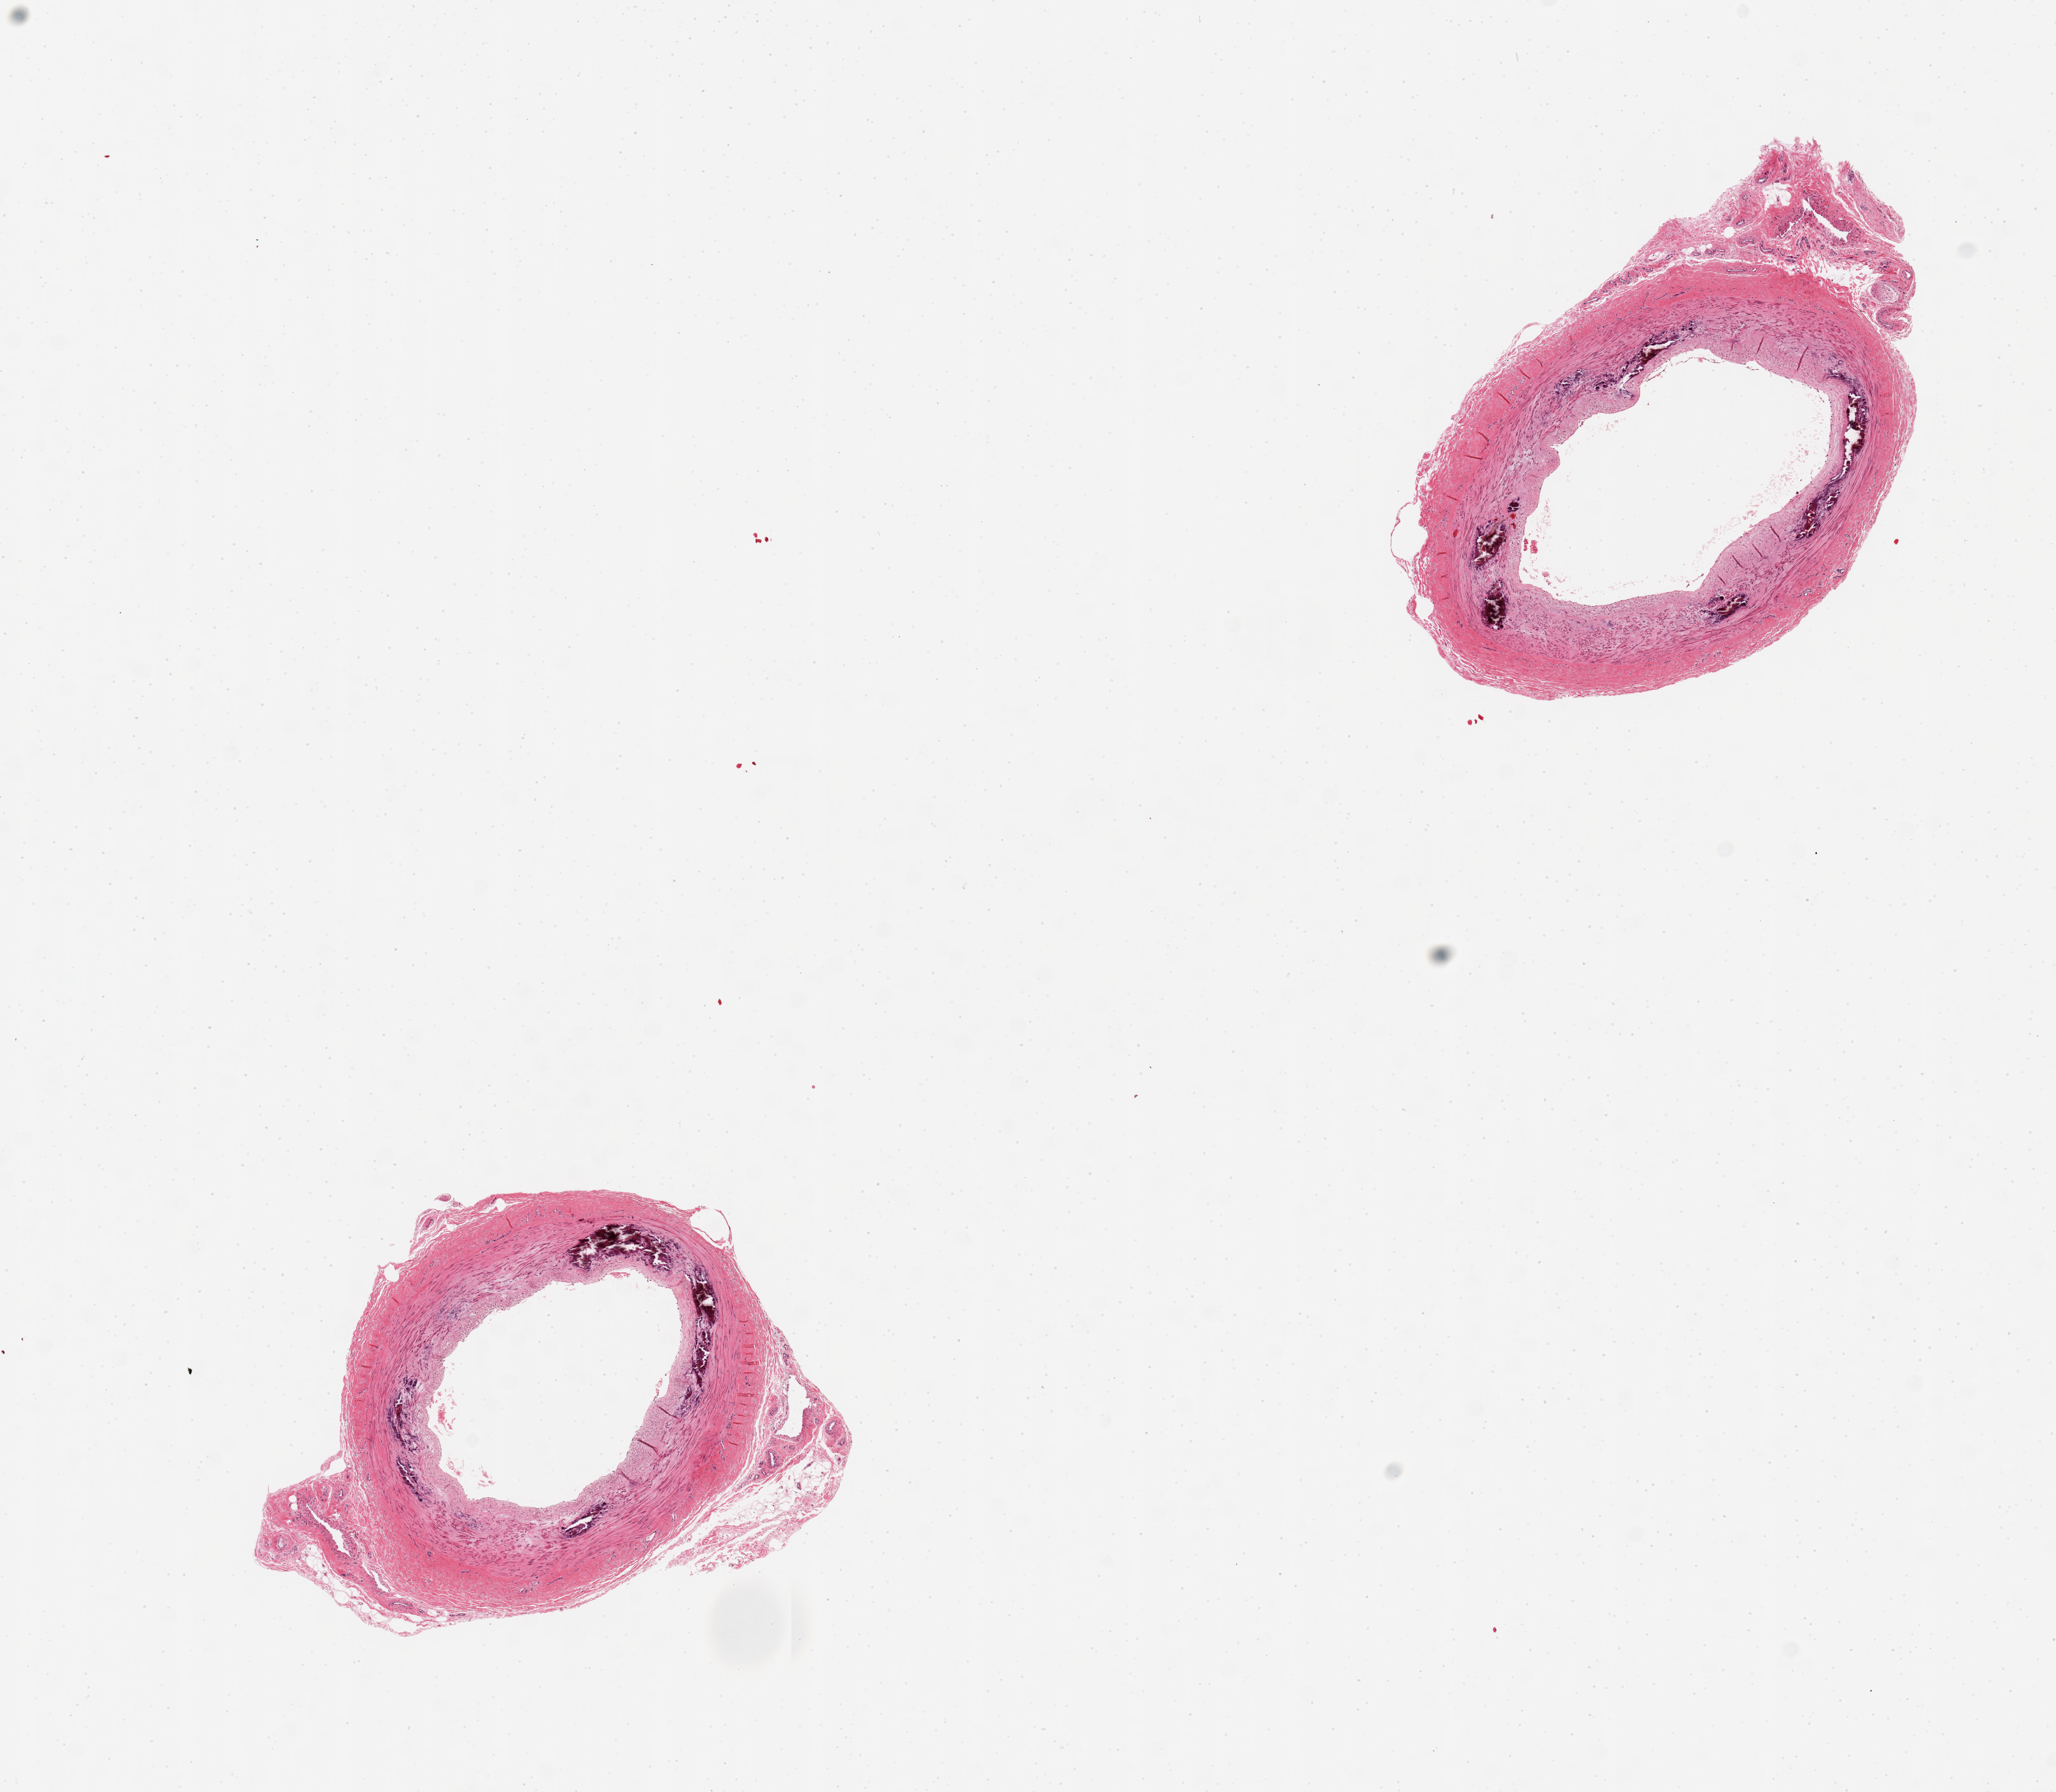
H&E whole-slide image, shown as a low-resolution overview of the whole scanned area (about 12.8 x 11.2 mm); PAXgene-fixed paraffin-embedded (PFPE) section; target tissue: tibial artery; tissue donor sample. Male donor.
* reviewer comment on this tissue sample: 2 pieces; prominent medial calcification; up to 1x0.5 mm perivascular fat